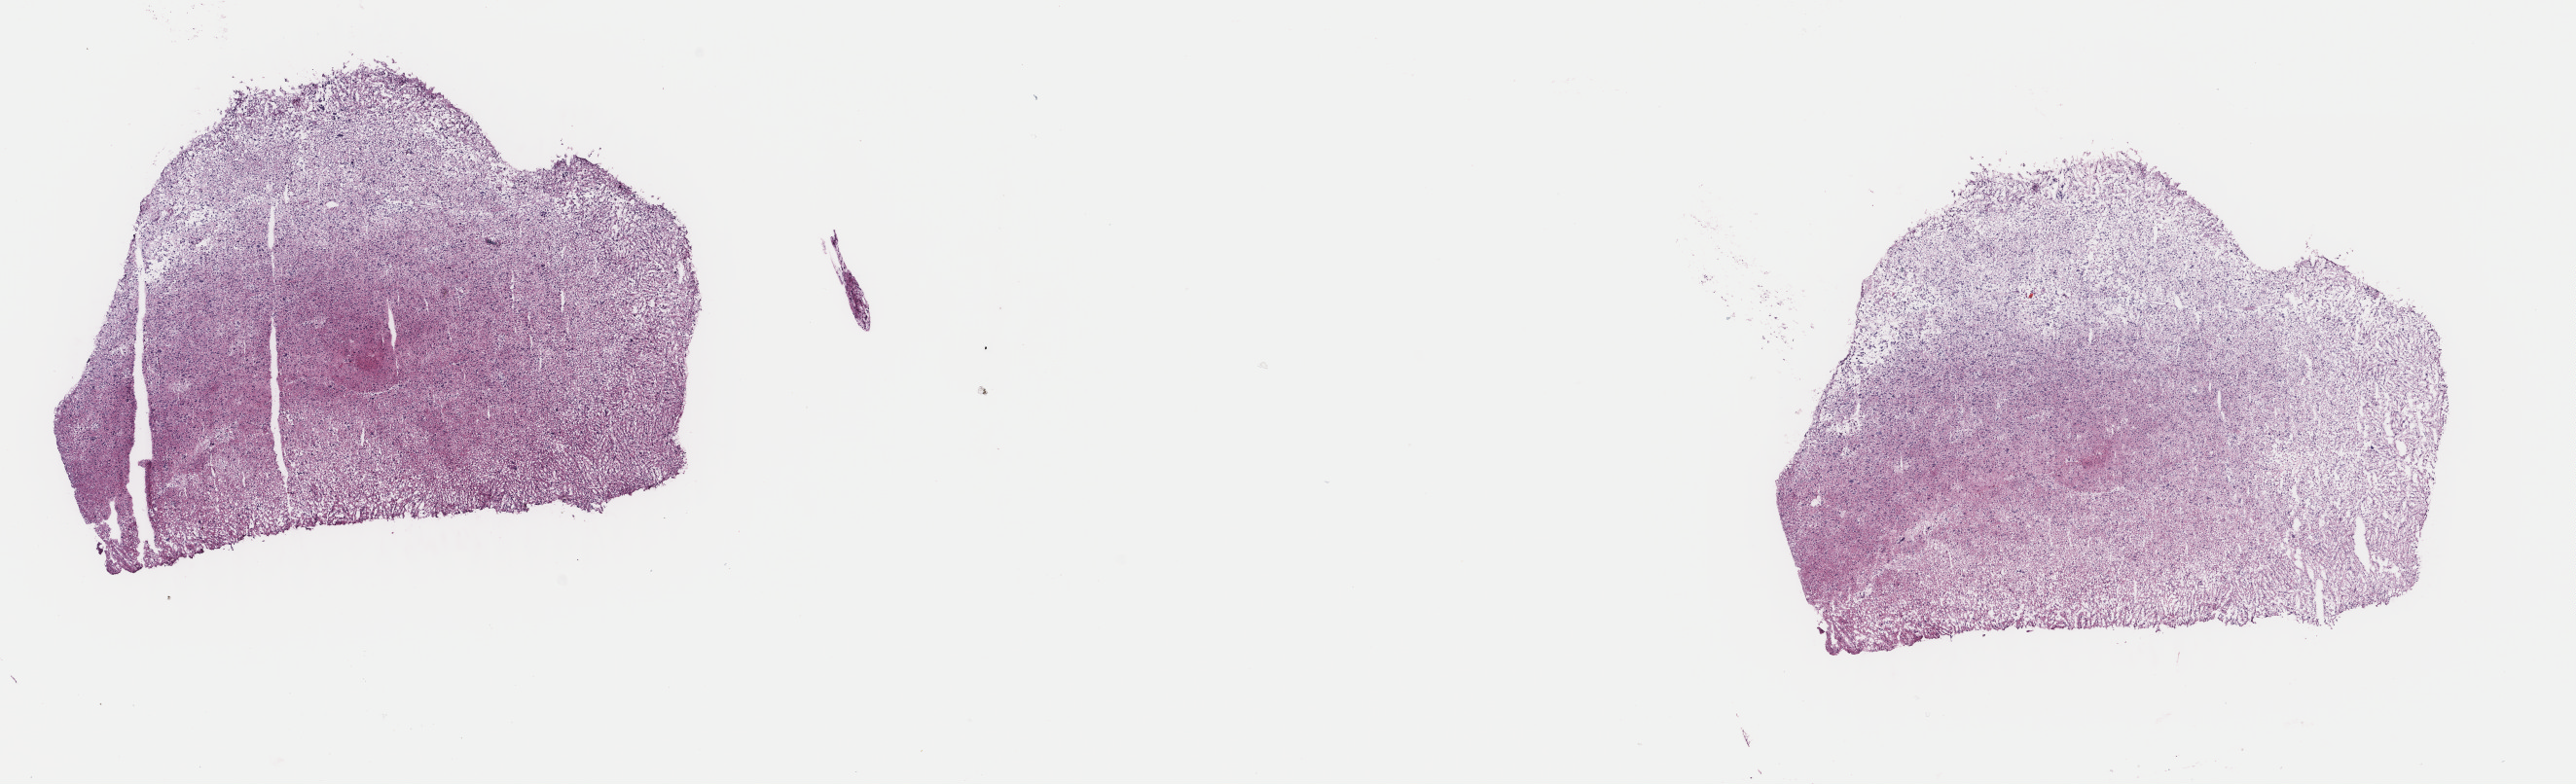
Hematoxylin and eosin (H&E) stained whole-slide image, whole scanned area (about 21.0 x 6.4 mm, from a 40x scan) shown as a low-resolution overview, frozen section from the top of the tissue portion, sample: primary tumour, brain. Female patient; age at initial diagnosis 33 years. Slide review estimates, as recorded: tumour cells 50%, tumour nuclei 90%.
Histologic diagnosis: Astrocytoma, anaplastic.